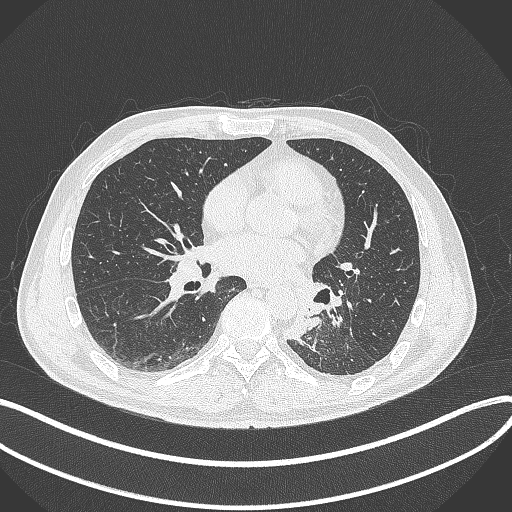
Chest CT, one axial slice; slice 145 of 329 in the series (ordered by position); reconstruction kernel B70f; 120 kVp; lung window (W 1500 / L -600 HU); 1 mm slice thickness; 512 × 512 image matrix. Patient: male, 59 years. Case-level facts recorded for this patient, not image findings: clinical TNM (as recorded): T2a N2 M0.
Outlined on this slice (rectangle marked by the reading radiologist):
- lung tumour (recorded histology: squamous cell carcinoma): bounding box [x1, y1, x2, y2] px = [276, 312, 329, 345]